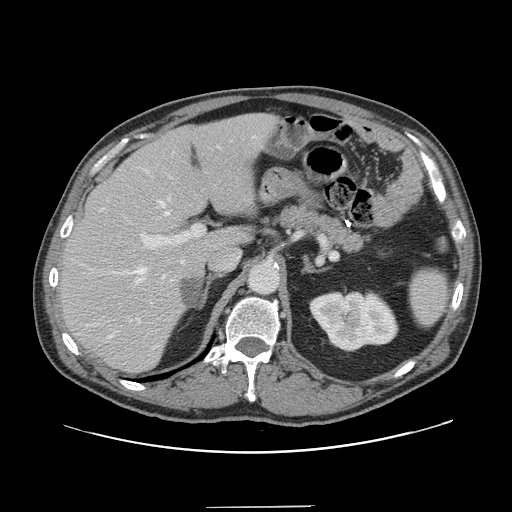
Contrast-enhanced abdominal CT, one axial slice; 120 kVp; intravenous contrast given; soft-tissue window (W 400 / L 40 HU); 2.5 mm slice thickness; 512 × 512 image matrix, field of view 397 × 397 mm. Male patient, age 64 years. From the clinical record (not read from this slice): diagnosis: colorectal cancer liver metastases, imaged before liver resection; multiple liver metastases: yes; largest metastasis: 3.5 cm; disease in both lobes: yes.
Outlined on this slice (expert manual segmentation):
- hepatic veins: box from (x=112, y=136) to (x=255, y=322) px
- liver: (x=62, y=115)–(x=273, y=371)
- planned liver remnant (the part of the liver to remain after resection): (x=62, y=115)–(x=270, y=371)
- portal vein (with intrahepatic branches): (x=138, y=225)–(x=205, y=323)
- liver metastasis: (x=181, y=279)–(x=201, y=308)